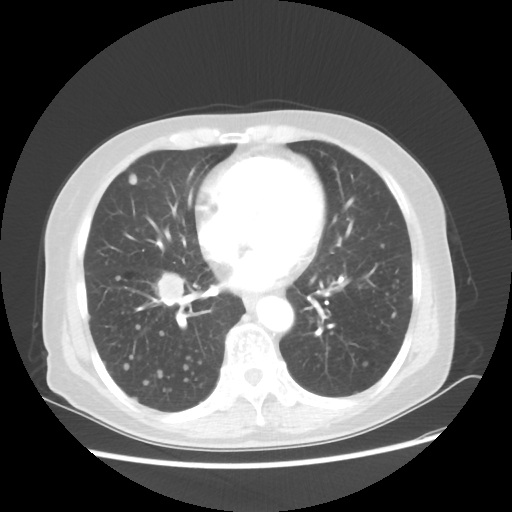
Chest CT, one axial slice. Slice 22 of 56 in the series (ordered by position). Reconstruction kernel STANDARD. Lung window (W 1500 / L -600 HU). 512 × 512 image matrix, field of view 360 × 360 mm. Female patient, age 68 years. Case-level facts recorded for this patient, not image findings: clinical TNM (as recorded): T1c N3 M0.
Outlined on this slice (rectangle marked by the reading radiologist):
- lung tumour (recorded histology: squamous cell carcinoma): bounding box <149,265,188,303> (left, top, right, bottom; pixels)